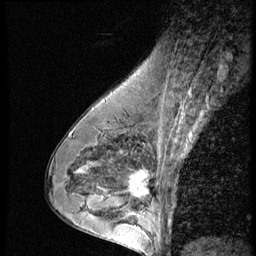
Breast MRI (dynamic contrast-enhanced), one sagittal slice. Position 34 of 56 along the scan axis. 3 images stored at this slice position (order not interpretable as contrast timing). 1.5 T. TE 4.2 ms, TR 9 ms. 256 × 256 image matrix. Female patient, age 43 years. Case-level facts recorded for this patient, not image findings: setting: breast cancer imaged before/during neoadjuvant chemotherapy; receptor status: HR-positive, HER2-negative.
Annotated regions visible in this slice (semi-automatically segmented with operator editing):
- analysis volume of interest (the breast-tissue region the enhancement analysis was run in; not a lesion): bounding box <120,160,163,207> (left, top, right, bottom; pixels)
- tumour enhancement mask (voxels above the 140 % enhancement threshold inside the analysis volume of interest): <126,172,150,197>